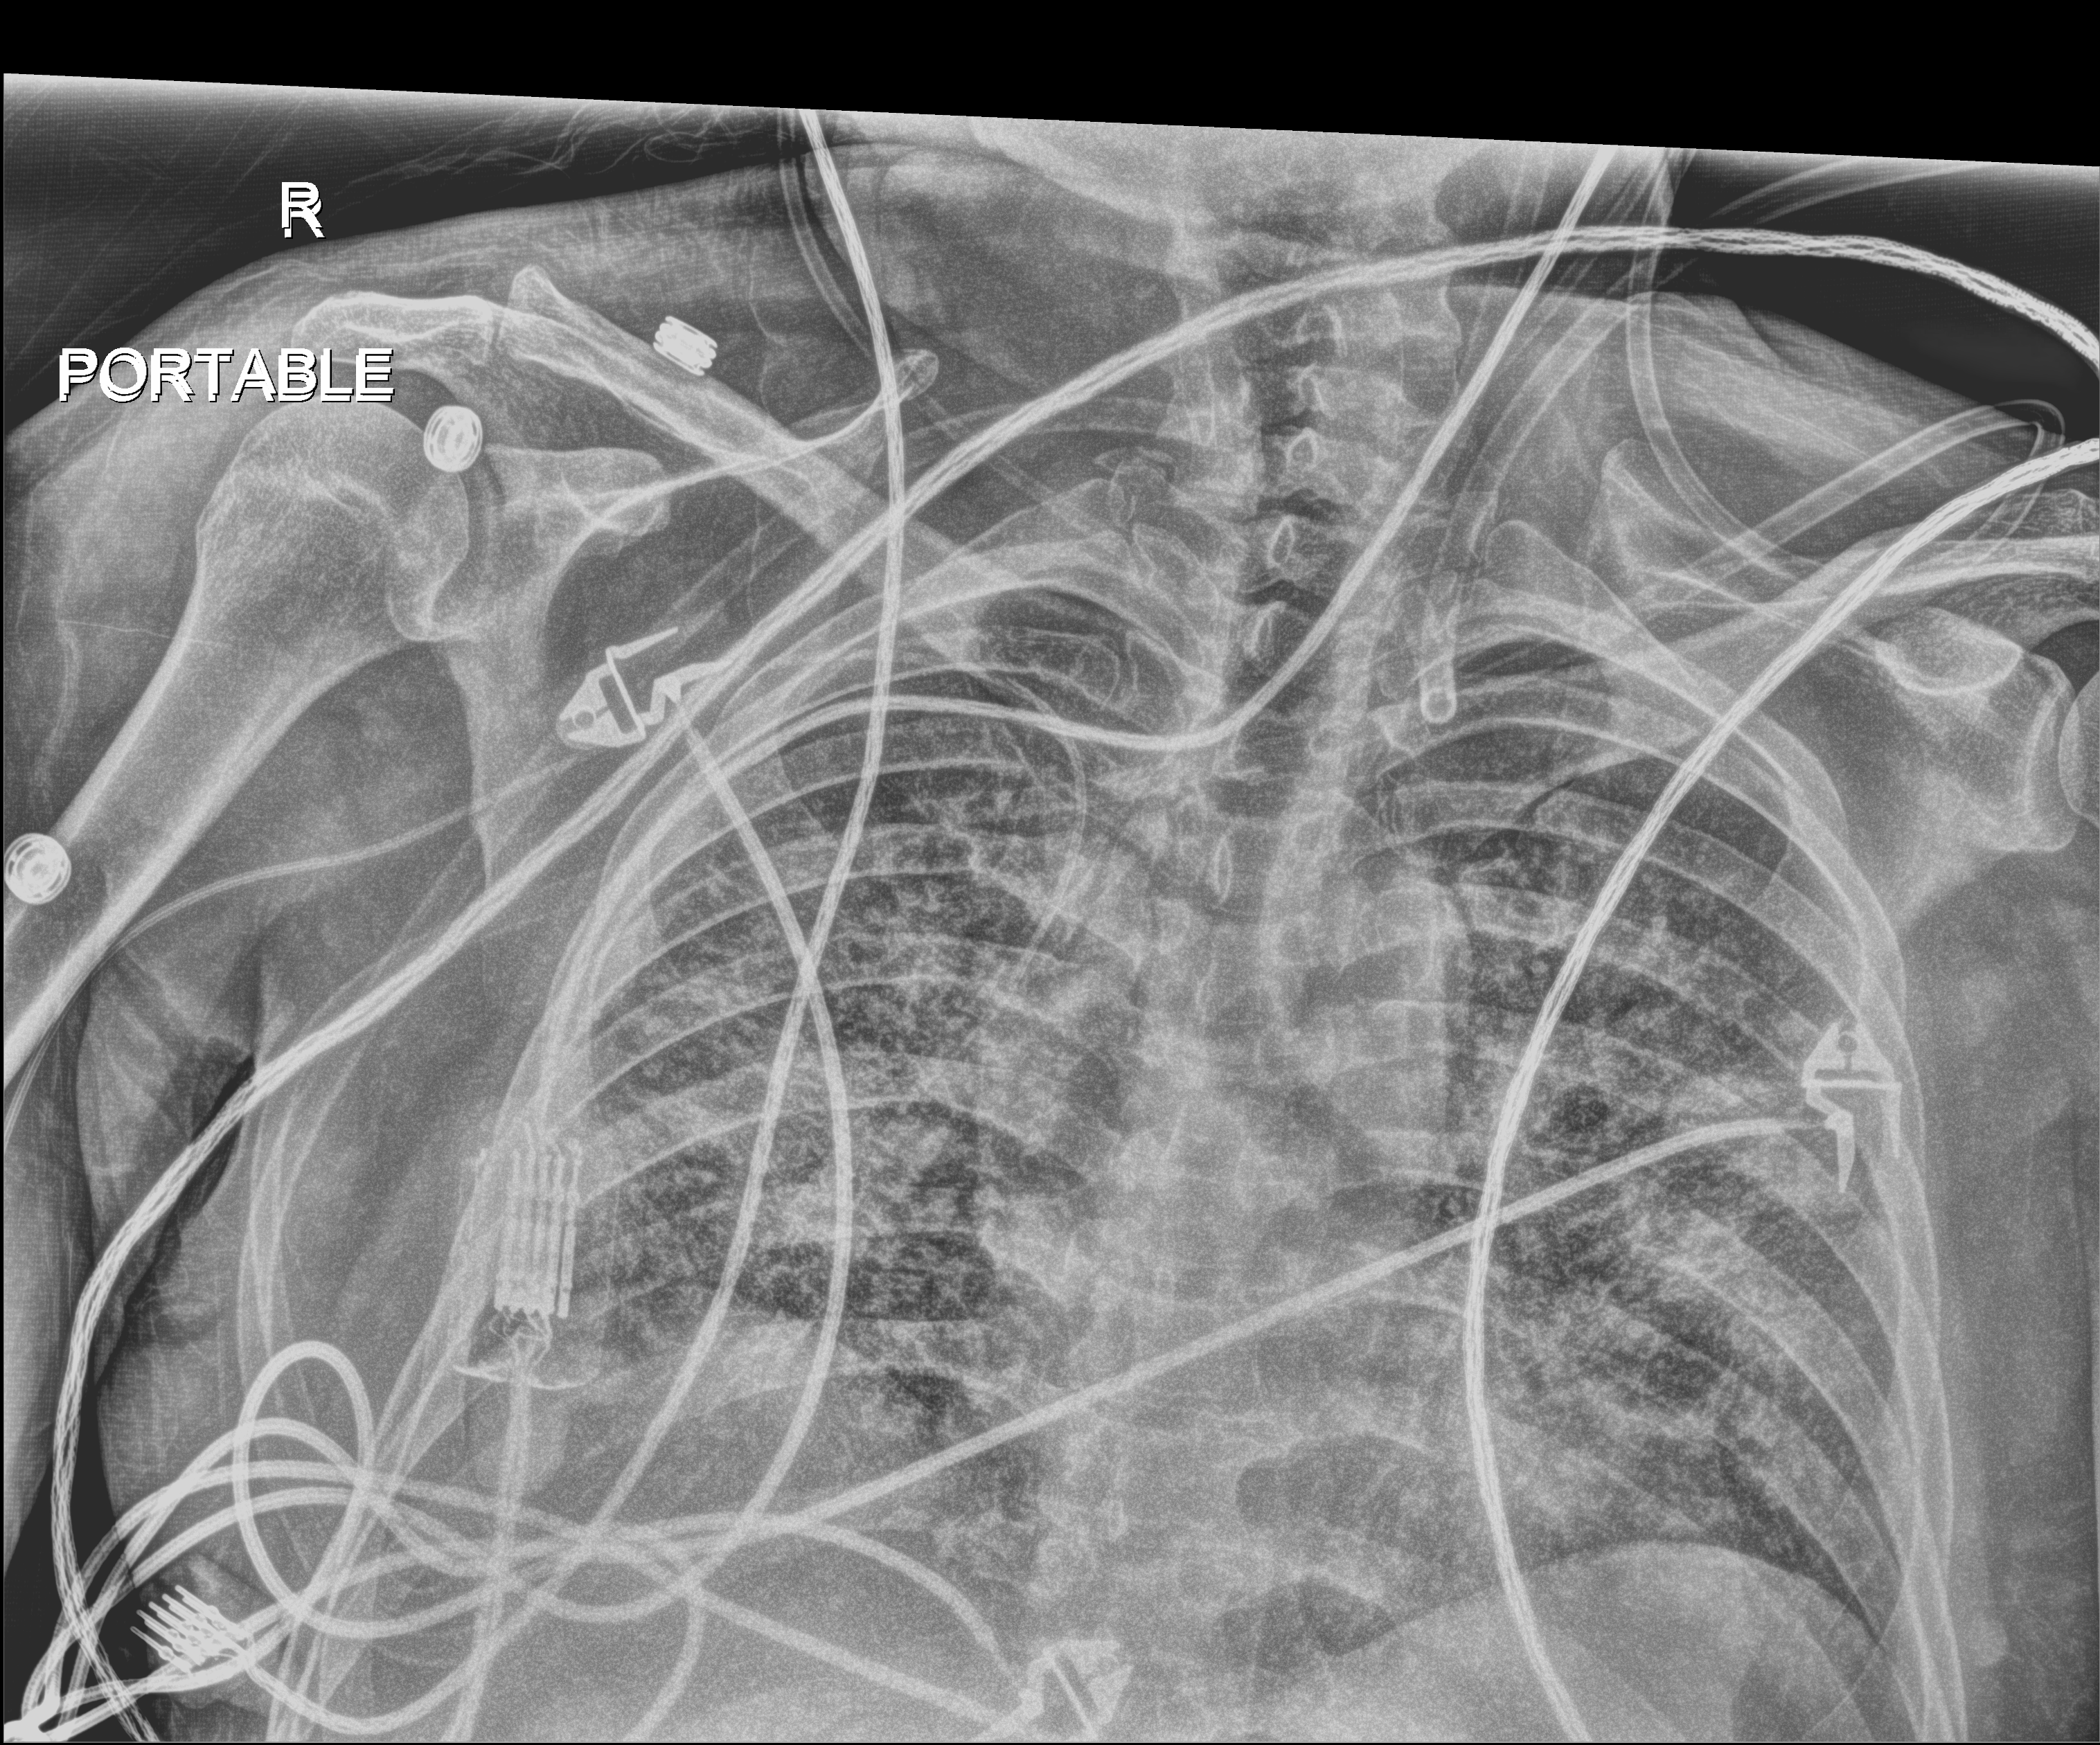
Chest X-ray, anteroposterior (AP) projection. Patient hospitalised with COVID-19; male, aged 18–59 years.
Admission-level facts for this patient (not findings on this image; timing relative to this image not recorded):
- mechanically ventilated during this hospital stay: yes
- length of hospital stay: 77 days
- hypertension (admission record): no